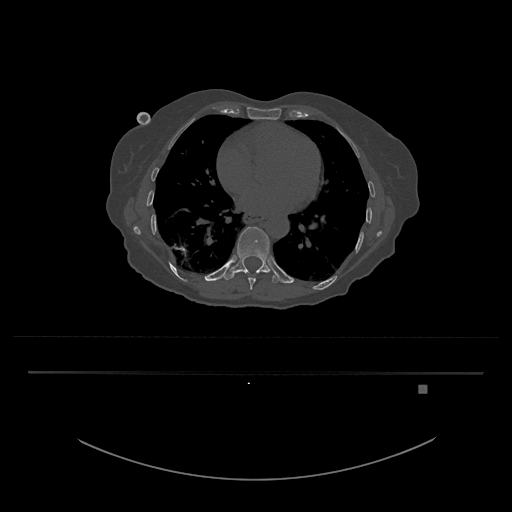
CT including the spine, one axial slice; slice 731 of 797 in the series (ordered by position); reconstruction kernel Br40s/3; 120 kVp; bone window (W 1800 / L 400 HU); 0.5 mm slice thickness; 512 × 512 image matrix. Patient: female, 57 years. Case-level facts recorded for this patient, not image findings: primary cancer: cervical.
Structures marked on this image (semi-automatically segmented with operator editing):
- T10 vertebra: box from (x=222, y=227) to (x=283, y=284) px
- T9 vertebra: (x=248, y=277)–(x=256, y=290)